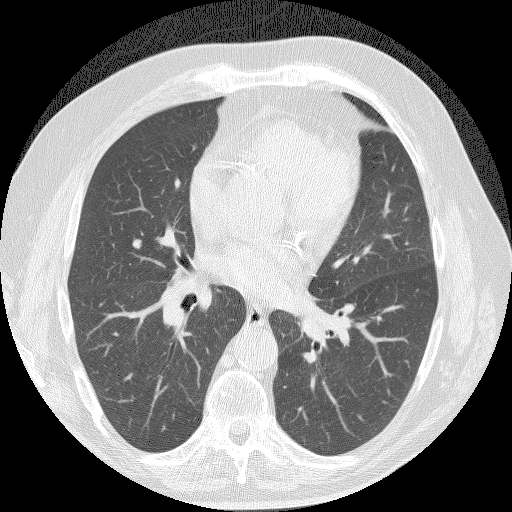
Axial slice from a low-dose chest CT screening exam; first (baseline) screen; lung window (W 1500 / L -600 HU); lung (sharp) reconstruction kernel (BONE); slice 79 of 145 in the series; 512 × 512 image matrix. Male participant, aged 61 years at enrolment. Current smoker at enrolment.
Expert reader's lesion annotation, box from (x=111, y=227) to (x=155, y=264) px. The screening reader recorded 3 non-calcified nodules or masses ≥4 mm on this exam (right upper lobe, right lower lobe); which of them this box marks is not recorded. Official screen result: positive, change unspecified: nodule(s) >= 4 mm or enlarging nodule(s), mass(es), or other non-specific abnormalities suspicious for lung cancer.